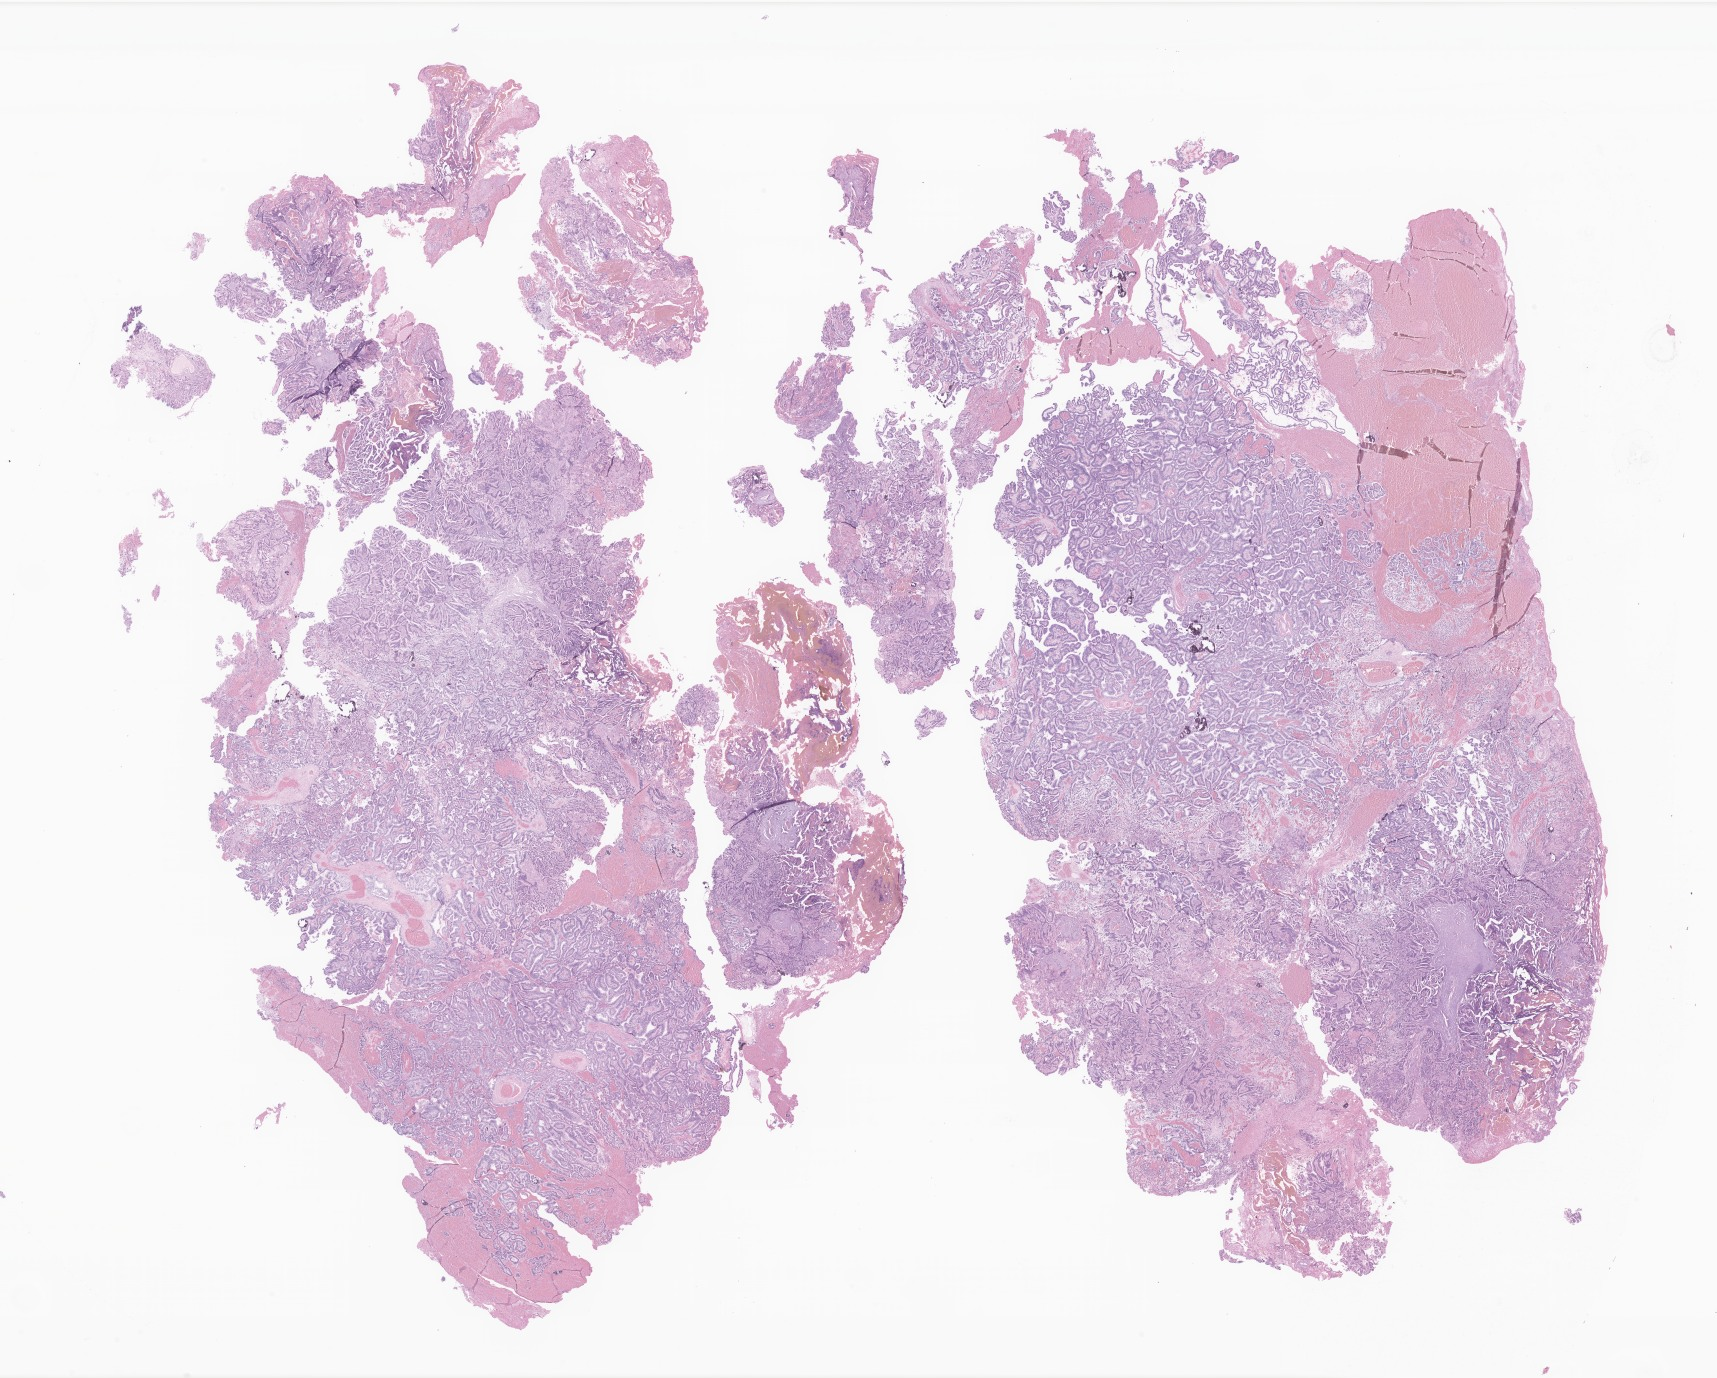
Digitized haematoxylin and eosin-stained section of tumor tissue from the brain, whole scanned area (about 29.0 x 23.2 mm) shown as a low-resolution overview; formalin-fixed paraffin-embedded section. Patient: male, age 75 months.
Recorded diagnosis: Choroid plexus papilloma, NOS.